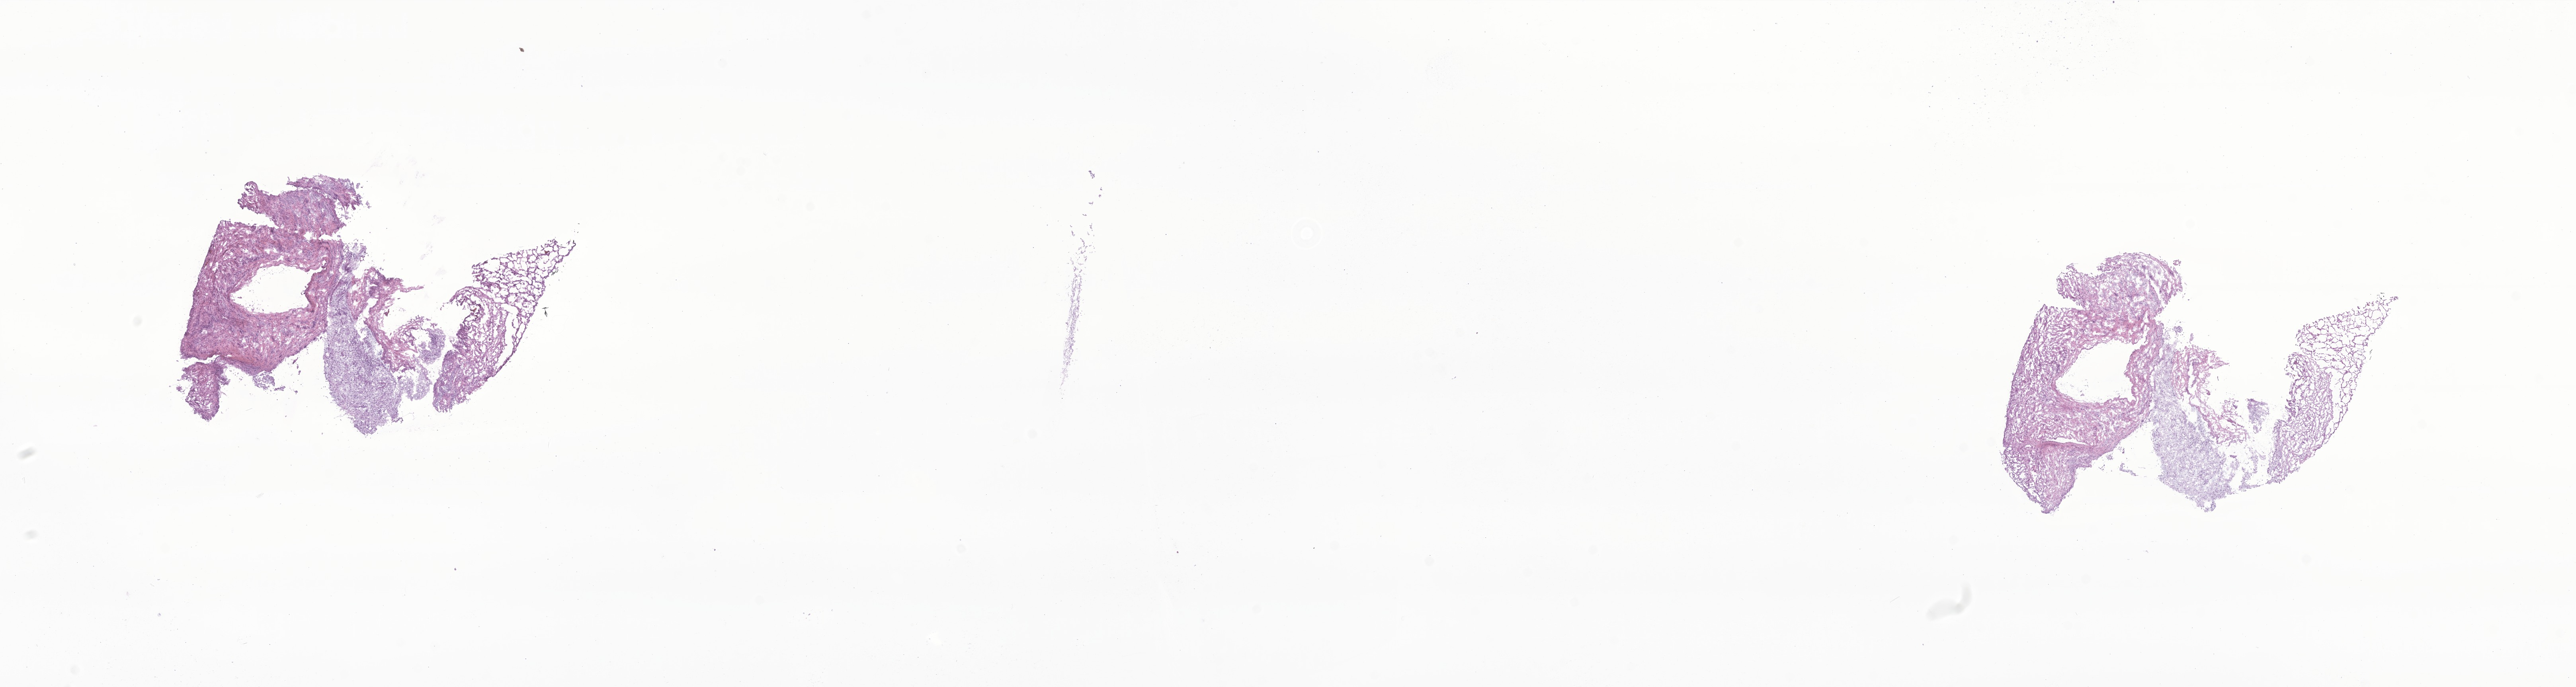
H&E whole-slide image of tumor tissue from the brain — shown as a low-resolution overview of the whole scanned area (about 27.3 x 7.3 mm), cryosection (OCT / tissue freezing medium). Male patient, age 741 days.
• diagnosis: Fibrillary astrocytoma